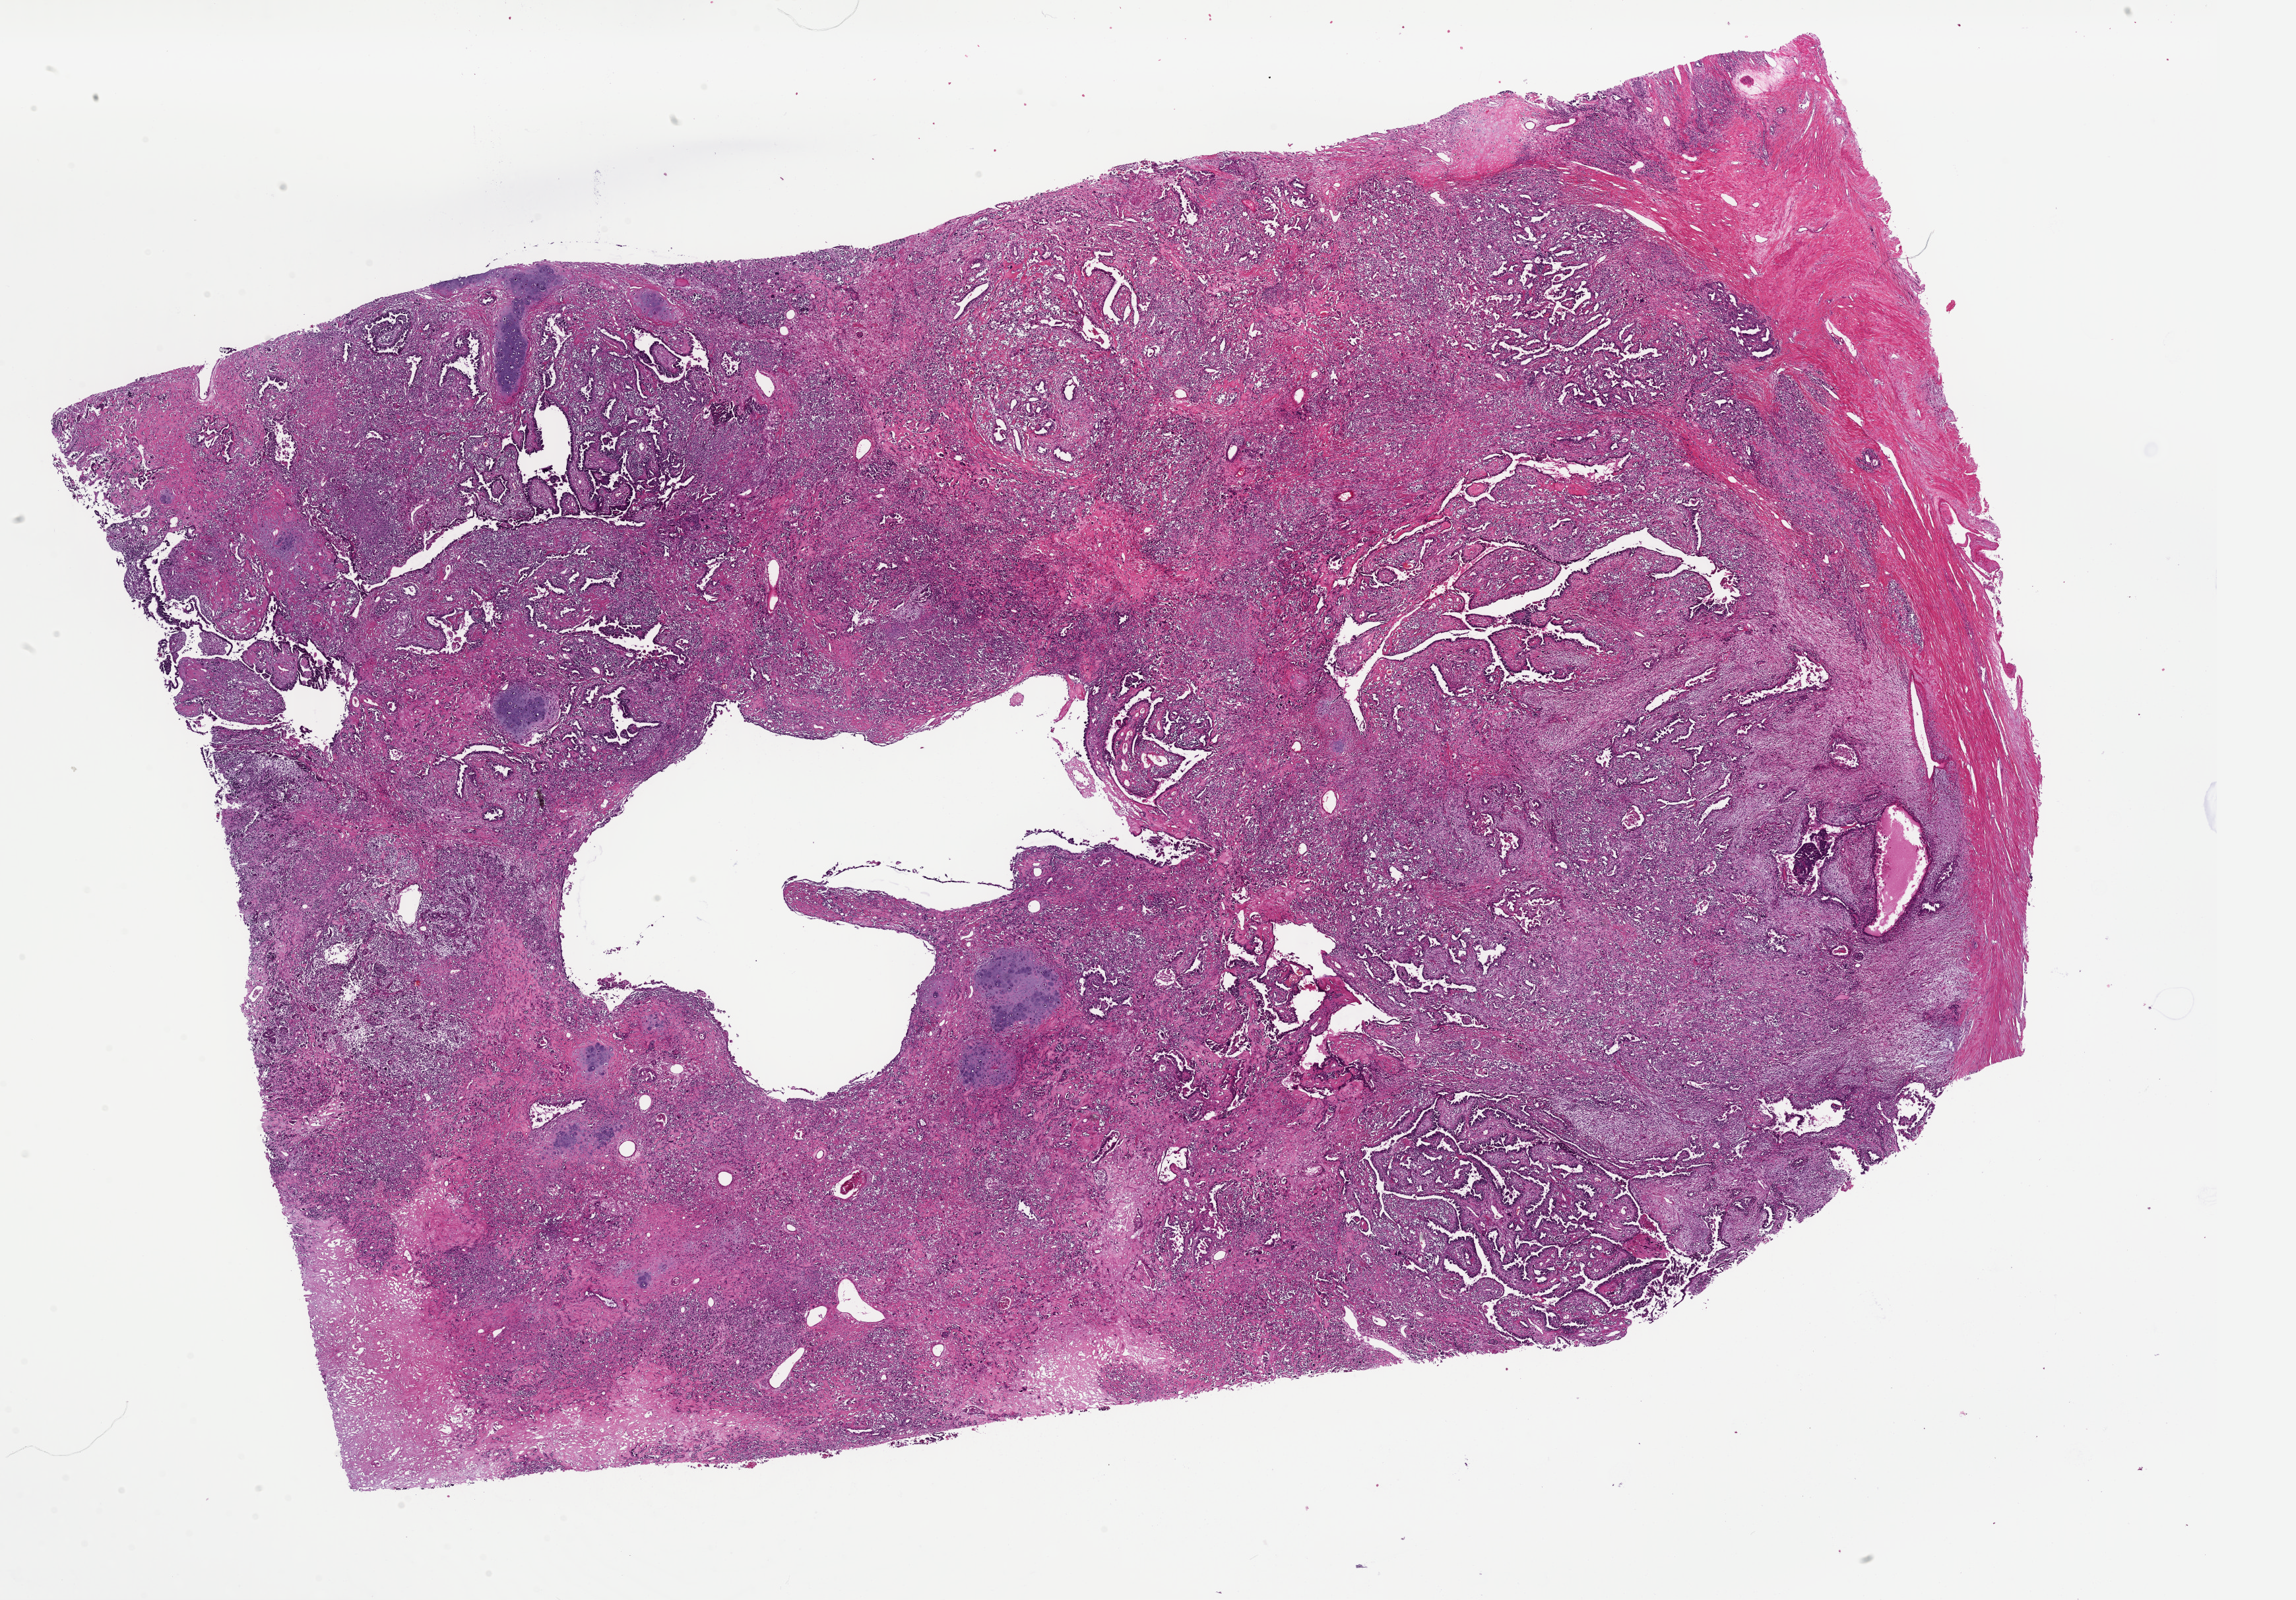
Digitized H&E-stained tissue section (whole slide) — whole scanned area (about 27.5 x 19.1 mm) shown as a low-resolution overview. Formalin-fixed paraffin-embedded (FFPE) diagnostic section. Uterus, primary tumour sample. Female, age 80 years at initial diagnosis.
• FIGO stage: IIIB
• histologic diagnosis: Carcinosarcoma, NOS